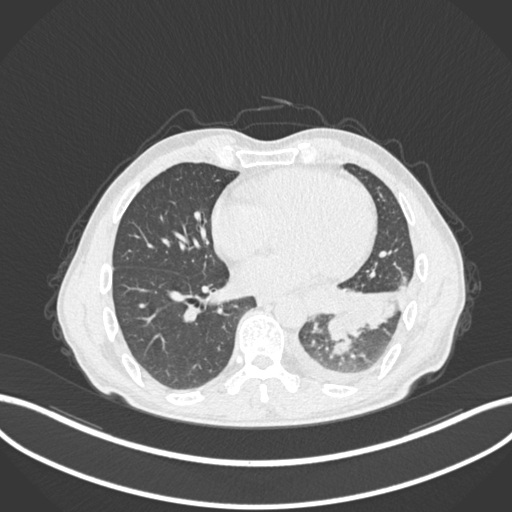
Chest CT, one axial slice; position 96 of 222 along the scan axis; 120 kVp; lung window (W 1500 / L -600 HU); 1 mm slice thickness; 512 × 512 image matrix, field of view 400 × 400 mm. Patient: male, 47 years. From the clinical record (not read from this slice): clinical TNM (as recorded): T3 N1 M1c.
Structures marked on this image (rectangle marked by the reading radiologist):
- lung tumour (recorded histology: small cell carcinoma): bounding box [x1, y1, x2, y2] px = [324, 310, 350, 344]